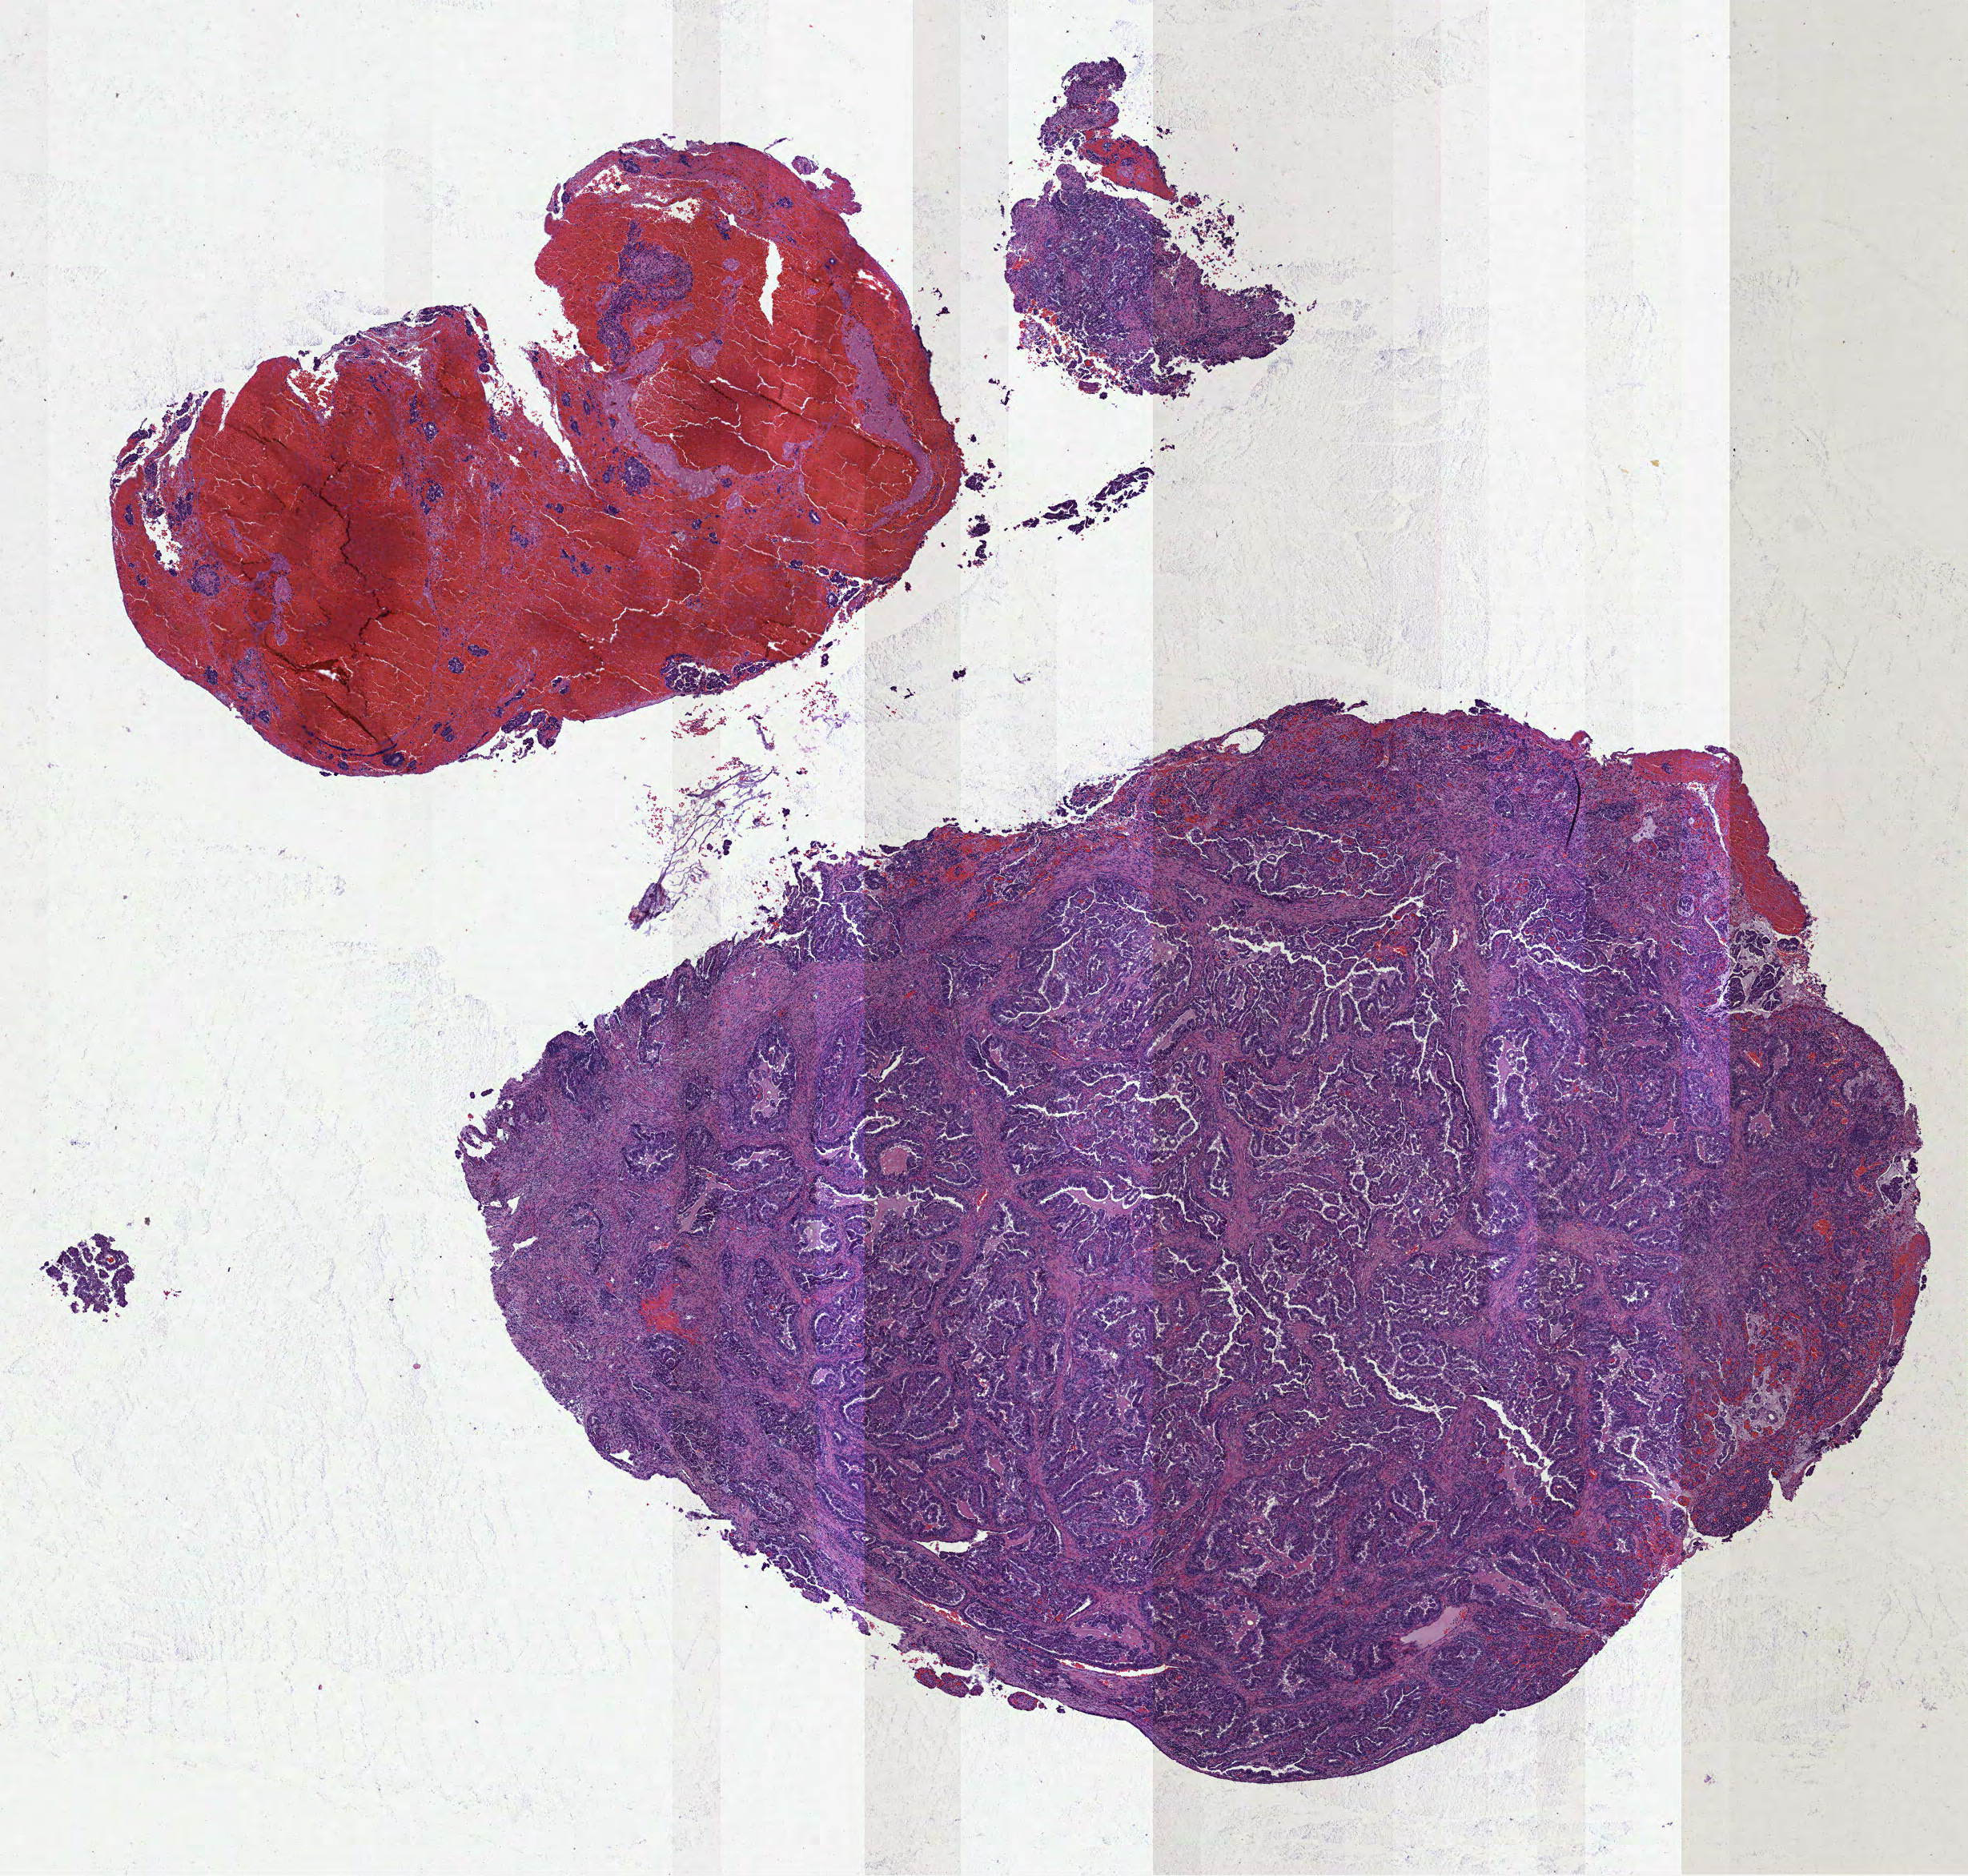
Digitized Hematoxylin and eosin (H&E) stained tissue section (whole slide), whole scanned area (about 9.9 x 9.4 mm, acquisition: 40x scan) shown as a low-resolution overview; formalin-fixed paraffin-embedded (FFPE) diagnostic section; primary tumour sample from the cervix. Female, age 49 years at initial diagnosis.
Pathologic diagnosis: Adenocarcinoma, endocervical type (endocervix).